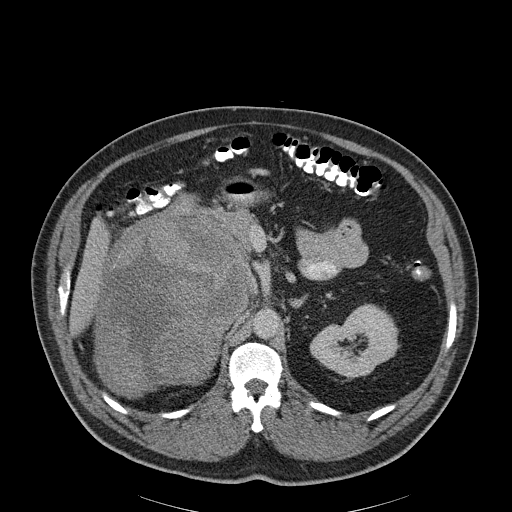
Contrast-enhanced abdominal CT, one axial slice; slice 126 of 186 in the series (ordered by position); 120 kVp; soft-tissue window (W 400 / L 40 HU); 3 mm slice thickness; 512 × 512 image matrix. Patient: male, 56 years. Case-level facts recorded for this patient, not image findings: diagnosis: adrenocortical carcinoma; tumour side: right adrenal; tumour size at pathology: 18 cm; Ki-67 index: 2 %; stage (as recorded): 3.
Structures marked on this image (semi-automatically segmented with operator editing):
- mass: bounding box [x1, y1, x2, y2] px = [97, 215, 247, 395]